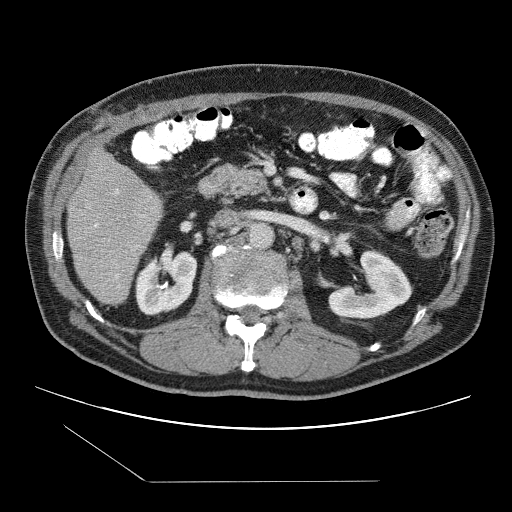
Contrast-enhanced abdominal CT (liver protocol), one axial slice; slice 34 of 109 in the series (ordered by position); reconstruction kernel STANDARD; one of 2 acquisitions stored at this slice position; soft-tissue window (W 400 / L 40 HU); 2.5 mm slice thickness; 512 × 512 image matrix, field of view 400 × 400 mm. From the clinical record (not read from this slice): diagnosis: hepatocellular carcinoma (patient treated with transarterial chemoembolisation; whether this scan precedes or follows treatment is not stated here); TNM stage (as recorded): Stage-IIIB; Child-Pugh class: A; tumour differentiation: well differentiated; tumour nodularity: multinodular.
Annotated regions visible in this slice (semi-automatic segmentation, software-assisted and operator-edited):
- liver parenchyma outside the tumour (the mass and vessels are separate outlines, so this box may not span the whole liver): bounding box [x1, y1, x2, y2] px = [66, 148, 162, 304]
- liver vessels: [94, 190, 144, 279]